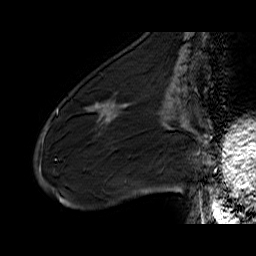
Breast MRI (dynamic contrast-enhanced), one sagittal slice. Position 21 of 60 along the scan axis. Dynamic contrast-enhanced series, time point 2 of 6 at this slice position (early post-contrast). 1.5 T. TE 6.5 ms, TR 32.9 ms. 4 mm slice thickness. 256 × 256 image matrix. Female patient. From the clinical record (not read from this slice): setting: breast cancer imaged before/during neoadjuvant chemotherapy; receptor status: HER2-positive.
Outlined on this slice (semi-automatic segmentation, software-assisted and operator-edited):
- analysis volume of interest (the breast-tissue region the enhancement analysis was run in; not a lesion): box from (x=72, y=88) to (x=133, y=137) px
- tumour enhancement mask (voxels above the 100 % enhancement threshold inside the analysis volume of interest): (x=86, y=109)–(x=88, y=111)